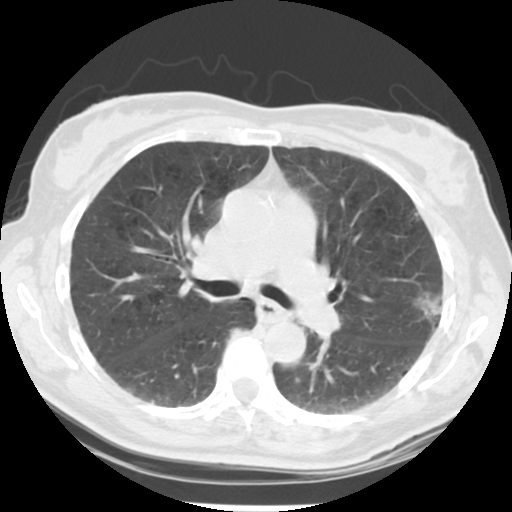
Low-dose screening chest CT, one axial slice. Position 133 of 223 along the scan axis. Reconstruction kernel STANDARD. Lung window (W 1500 / L -600 HU). 2.5 mm slice thickness. 512 × 512 image matrix, field of view 302 × 302 mm.
Outlined on this slice (outlined manually by an expert reader):
- lesion 1 (tumor, upper lobe of left lung): bounding box (x1, y1, x2, y2) in pixels: (415, 293, 442, 321)